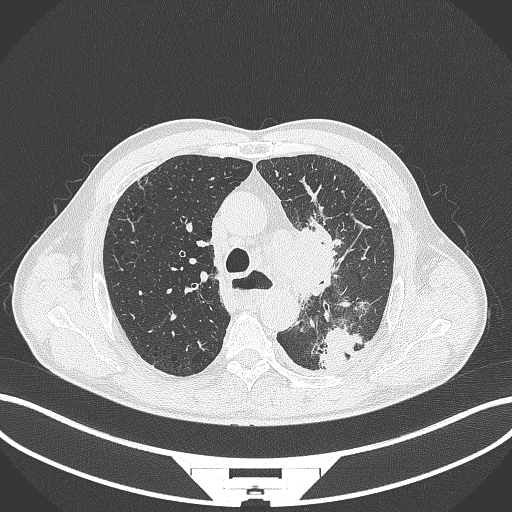
Chest CT, one axial slice. Position 270 of 411 along the scan axis. Reconstruction kernel B70f. 120 kVp. Lung window (W 1500 / L -600 HU). 1 mm slice thickness. 512 × 512 image matrix, field of view 400 × 400 mm. Patient: male, 57 years. From the clinical record (not read from this slice): clinical TNM (as recorded): T2a N1 M0.
Outlined on this slice (rectangle marked by the reading radiologist):
- lung tumour (recorded histology: squamous cell carcinoma): box from (x=287, y=218) to (x=344, y=303) px